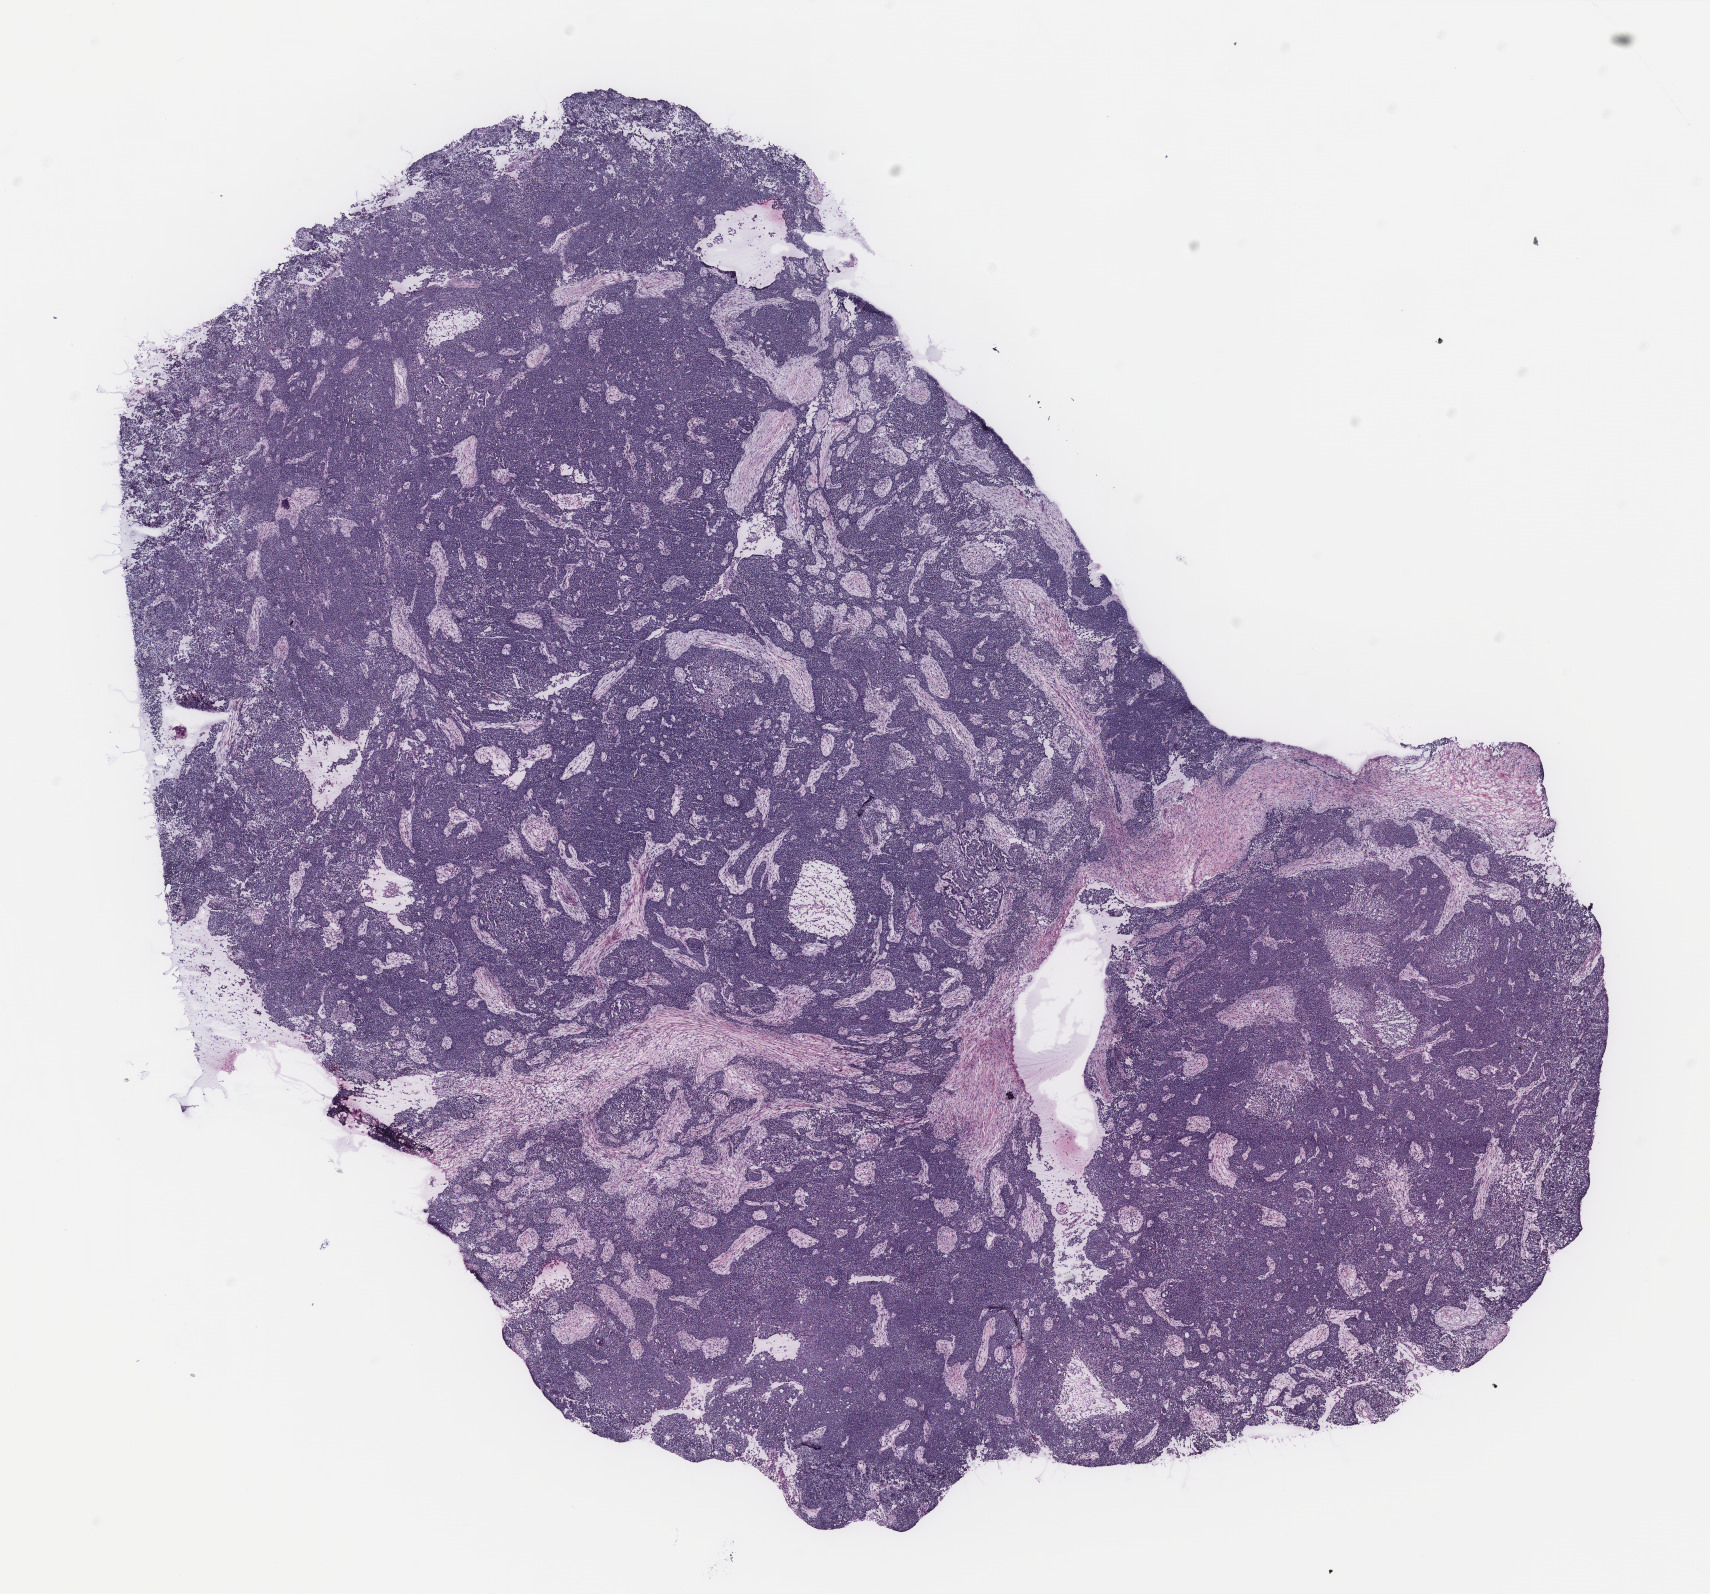
Digitized H&E-stained tissue section (whole slide) — whole scanned area (about 13.7 x 12.8 mm, from a 40x scan) shown as a low-resolution overview, tumour tissue sample, ovary. Patient: female, age 54 years.
- histologic diagnosis: Serous adenocarcinoma, NOS (peritoneum, NOS)
- primary tumour site (as recorded): peritoneum